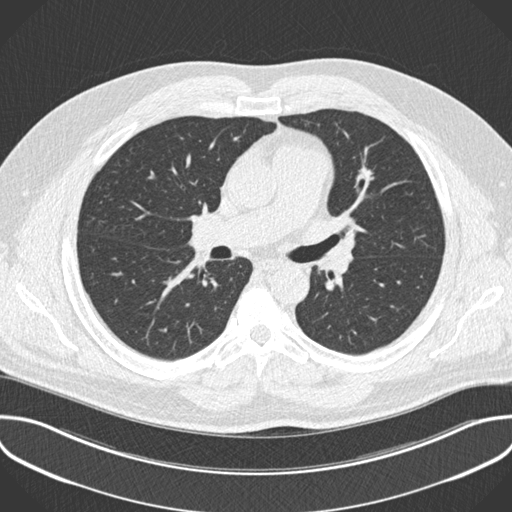
Chest CT (low-dose screening protocol), one axial image. First (baseline) screen. Lung window (W 1500 / L -600 HU). 2 mm slice thickness. Standard (soft-tissue) reconstruction kernel (B30f). Slice 76 of 201 in the series. 512 × 512 image matrix, field of view 386 × 386 mm. Male, age 55 years at enrolment.
Expert-annotated lung lesion, box from (x=344, y=158) to (x=391, y=193) px. The exam's reader record, not a measurement of the box and not confirmed to be the same lesion: non-calcified nodule or mass ≥4 mm, lingula, 13 × 12 mm, spiculated (stellate) margins, soft tissue attenuation. Official screen result: positive, change unspecified: nodule(s) >= 4 mm or enlarging nodule(s), mass(es), or other non-specific abnormalities suspicious for lung cancer.